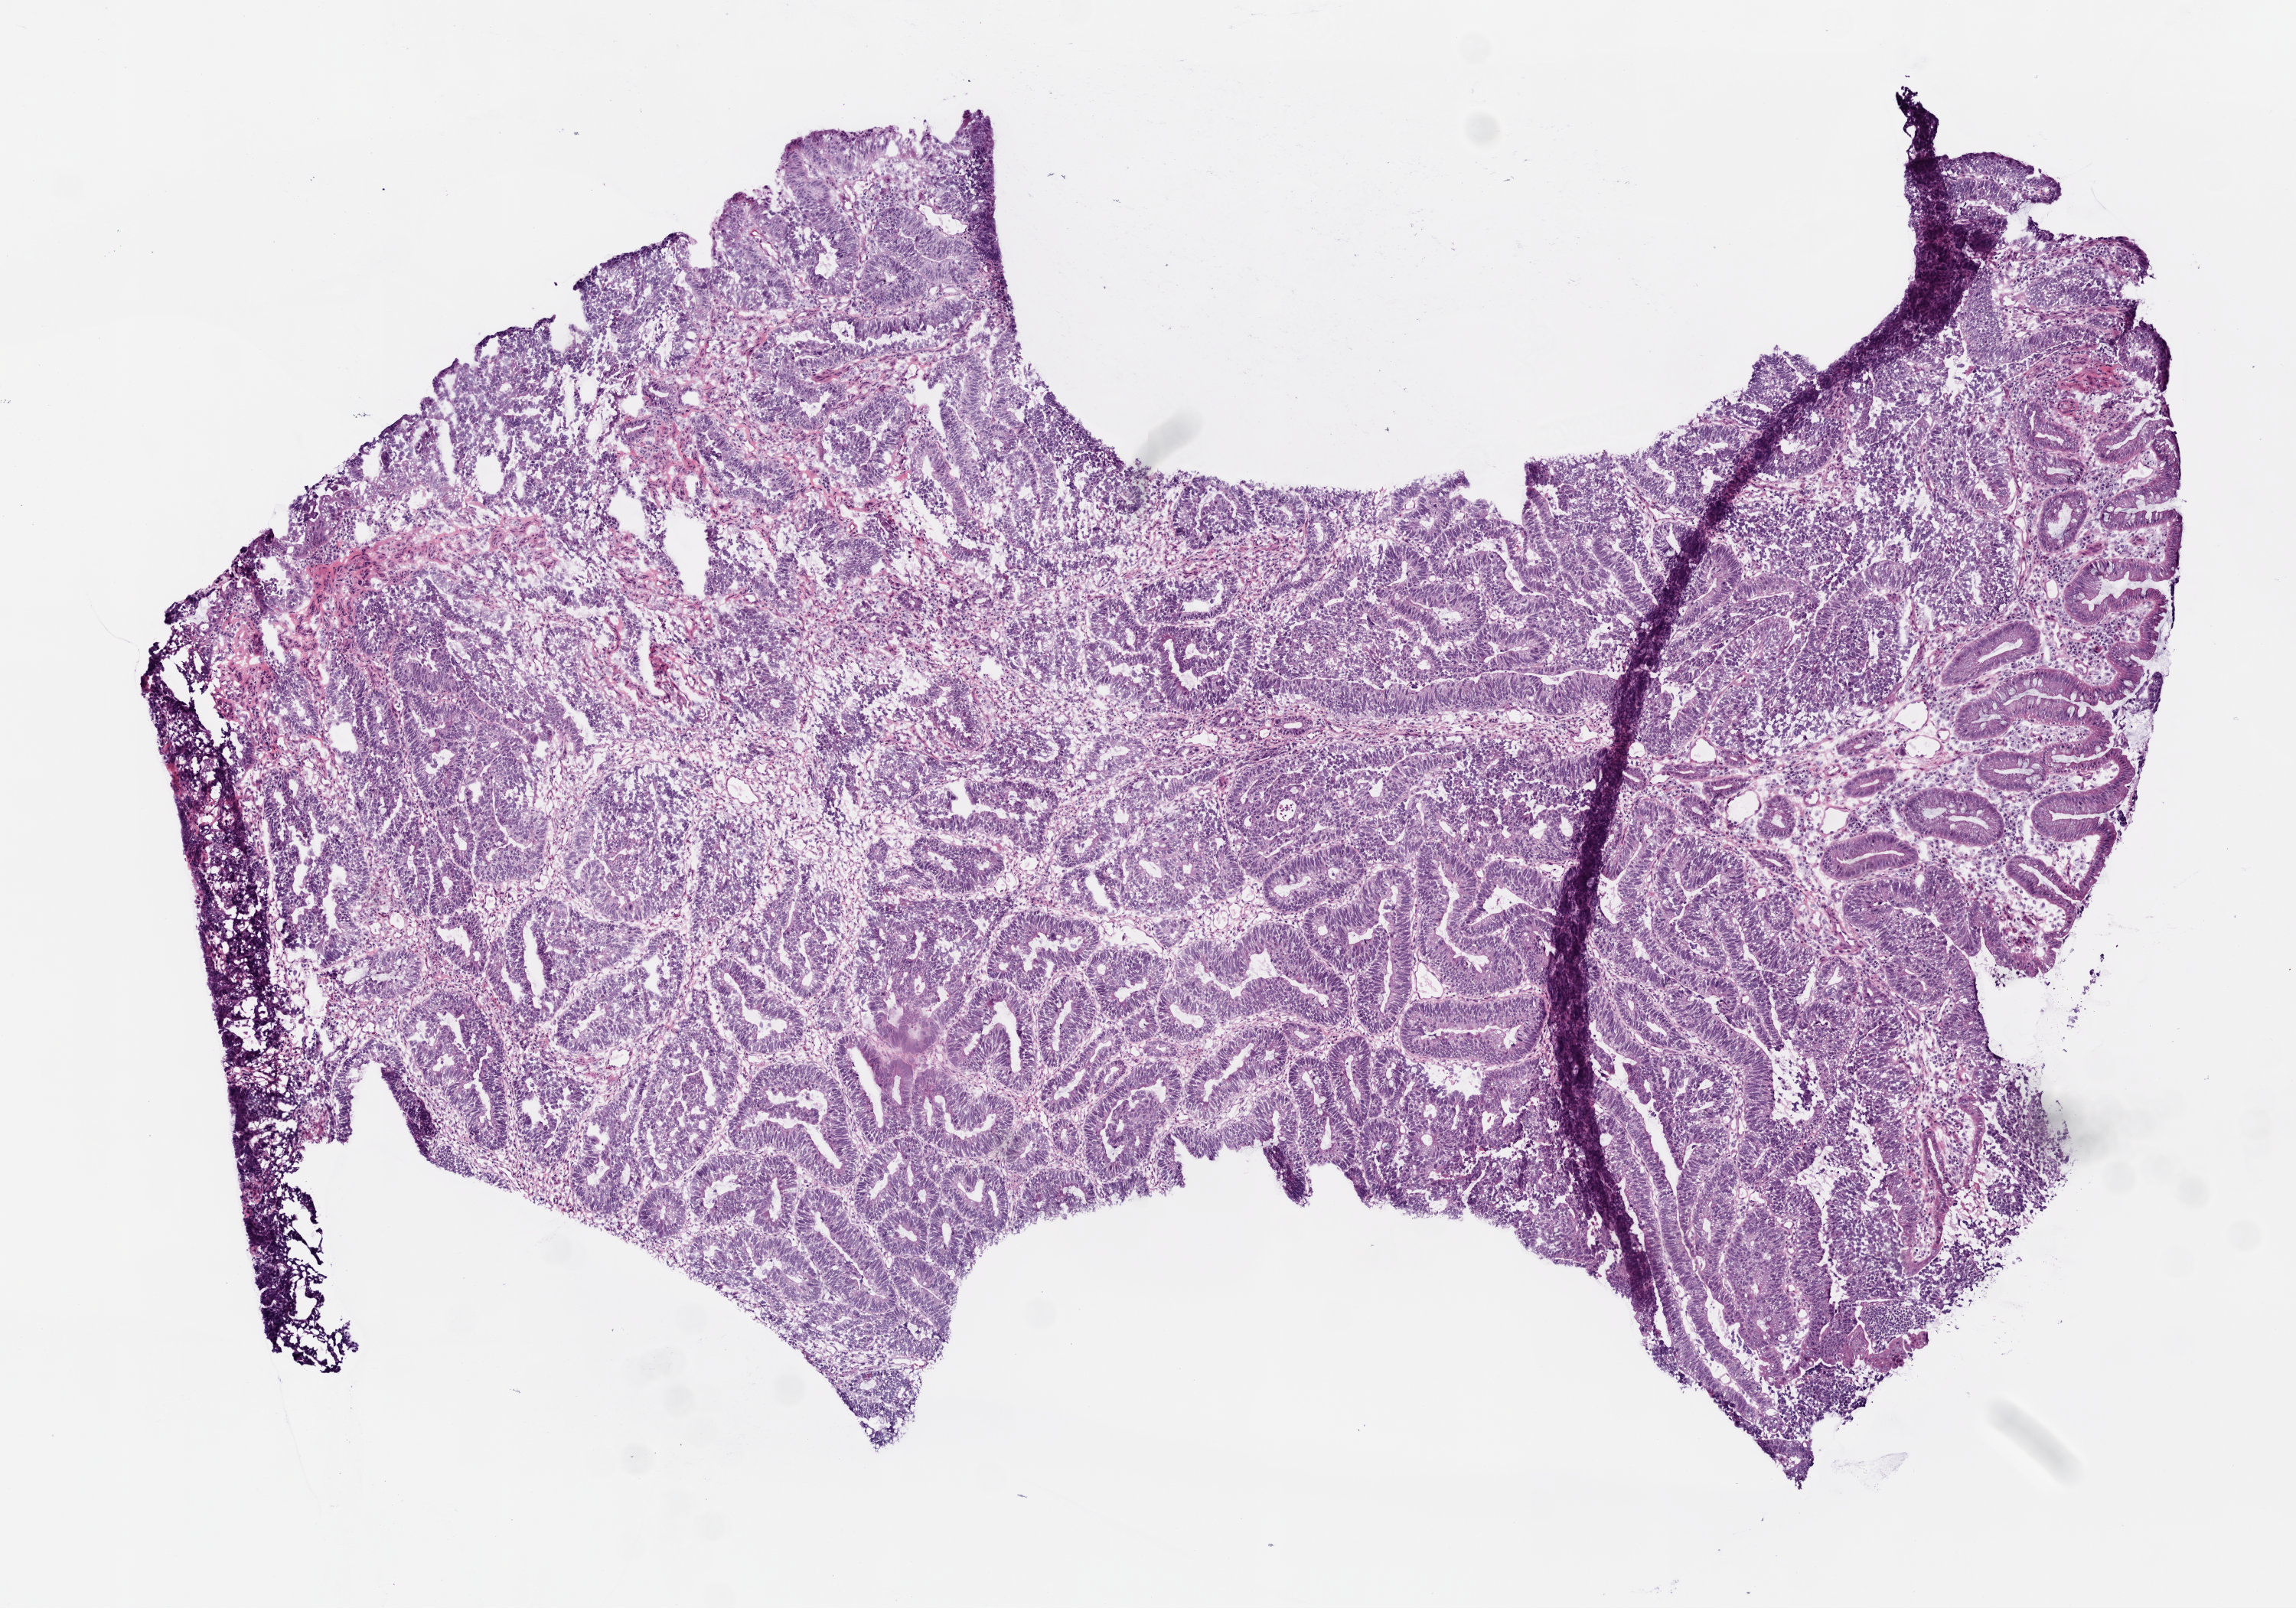
H&E whole-slide image, whole scanned area (about 6.0 x 4.2 mm) shown as a low-resolution overview; frozen section from the bottom of the tissue portion; sample: primary tumour, colon. Male, age 38 years at initial diagnosis. Composition of this section per pathologist review: tumour cells 74%, tumour nuclei 80%, normal cells 5%, stromal cells 20%, necrosis 1%.
Diagnosis: Adenocarcinoma, NOS. Lymph nodes positive (case pathology): 5 of 31 examined. AJCC pathologic stage: IIIB.